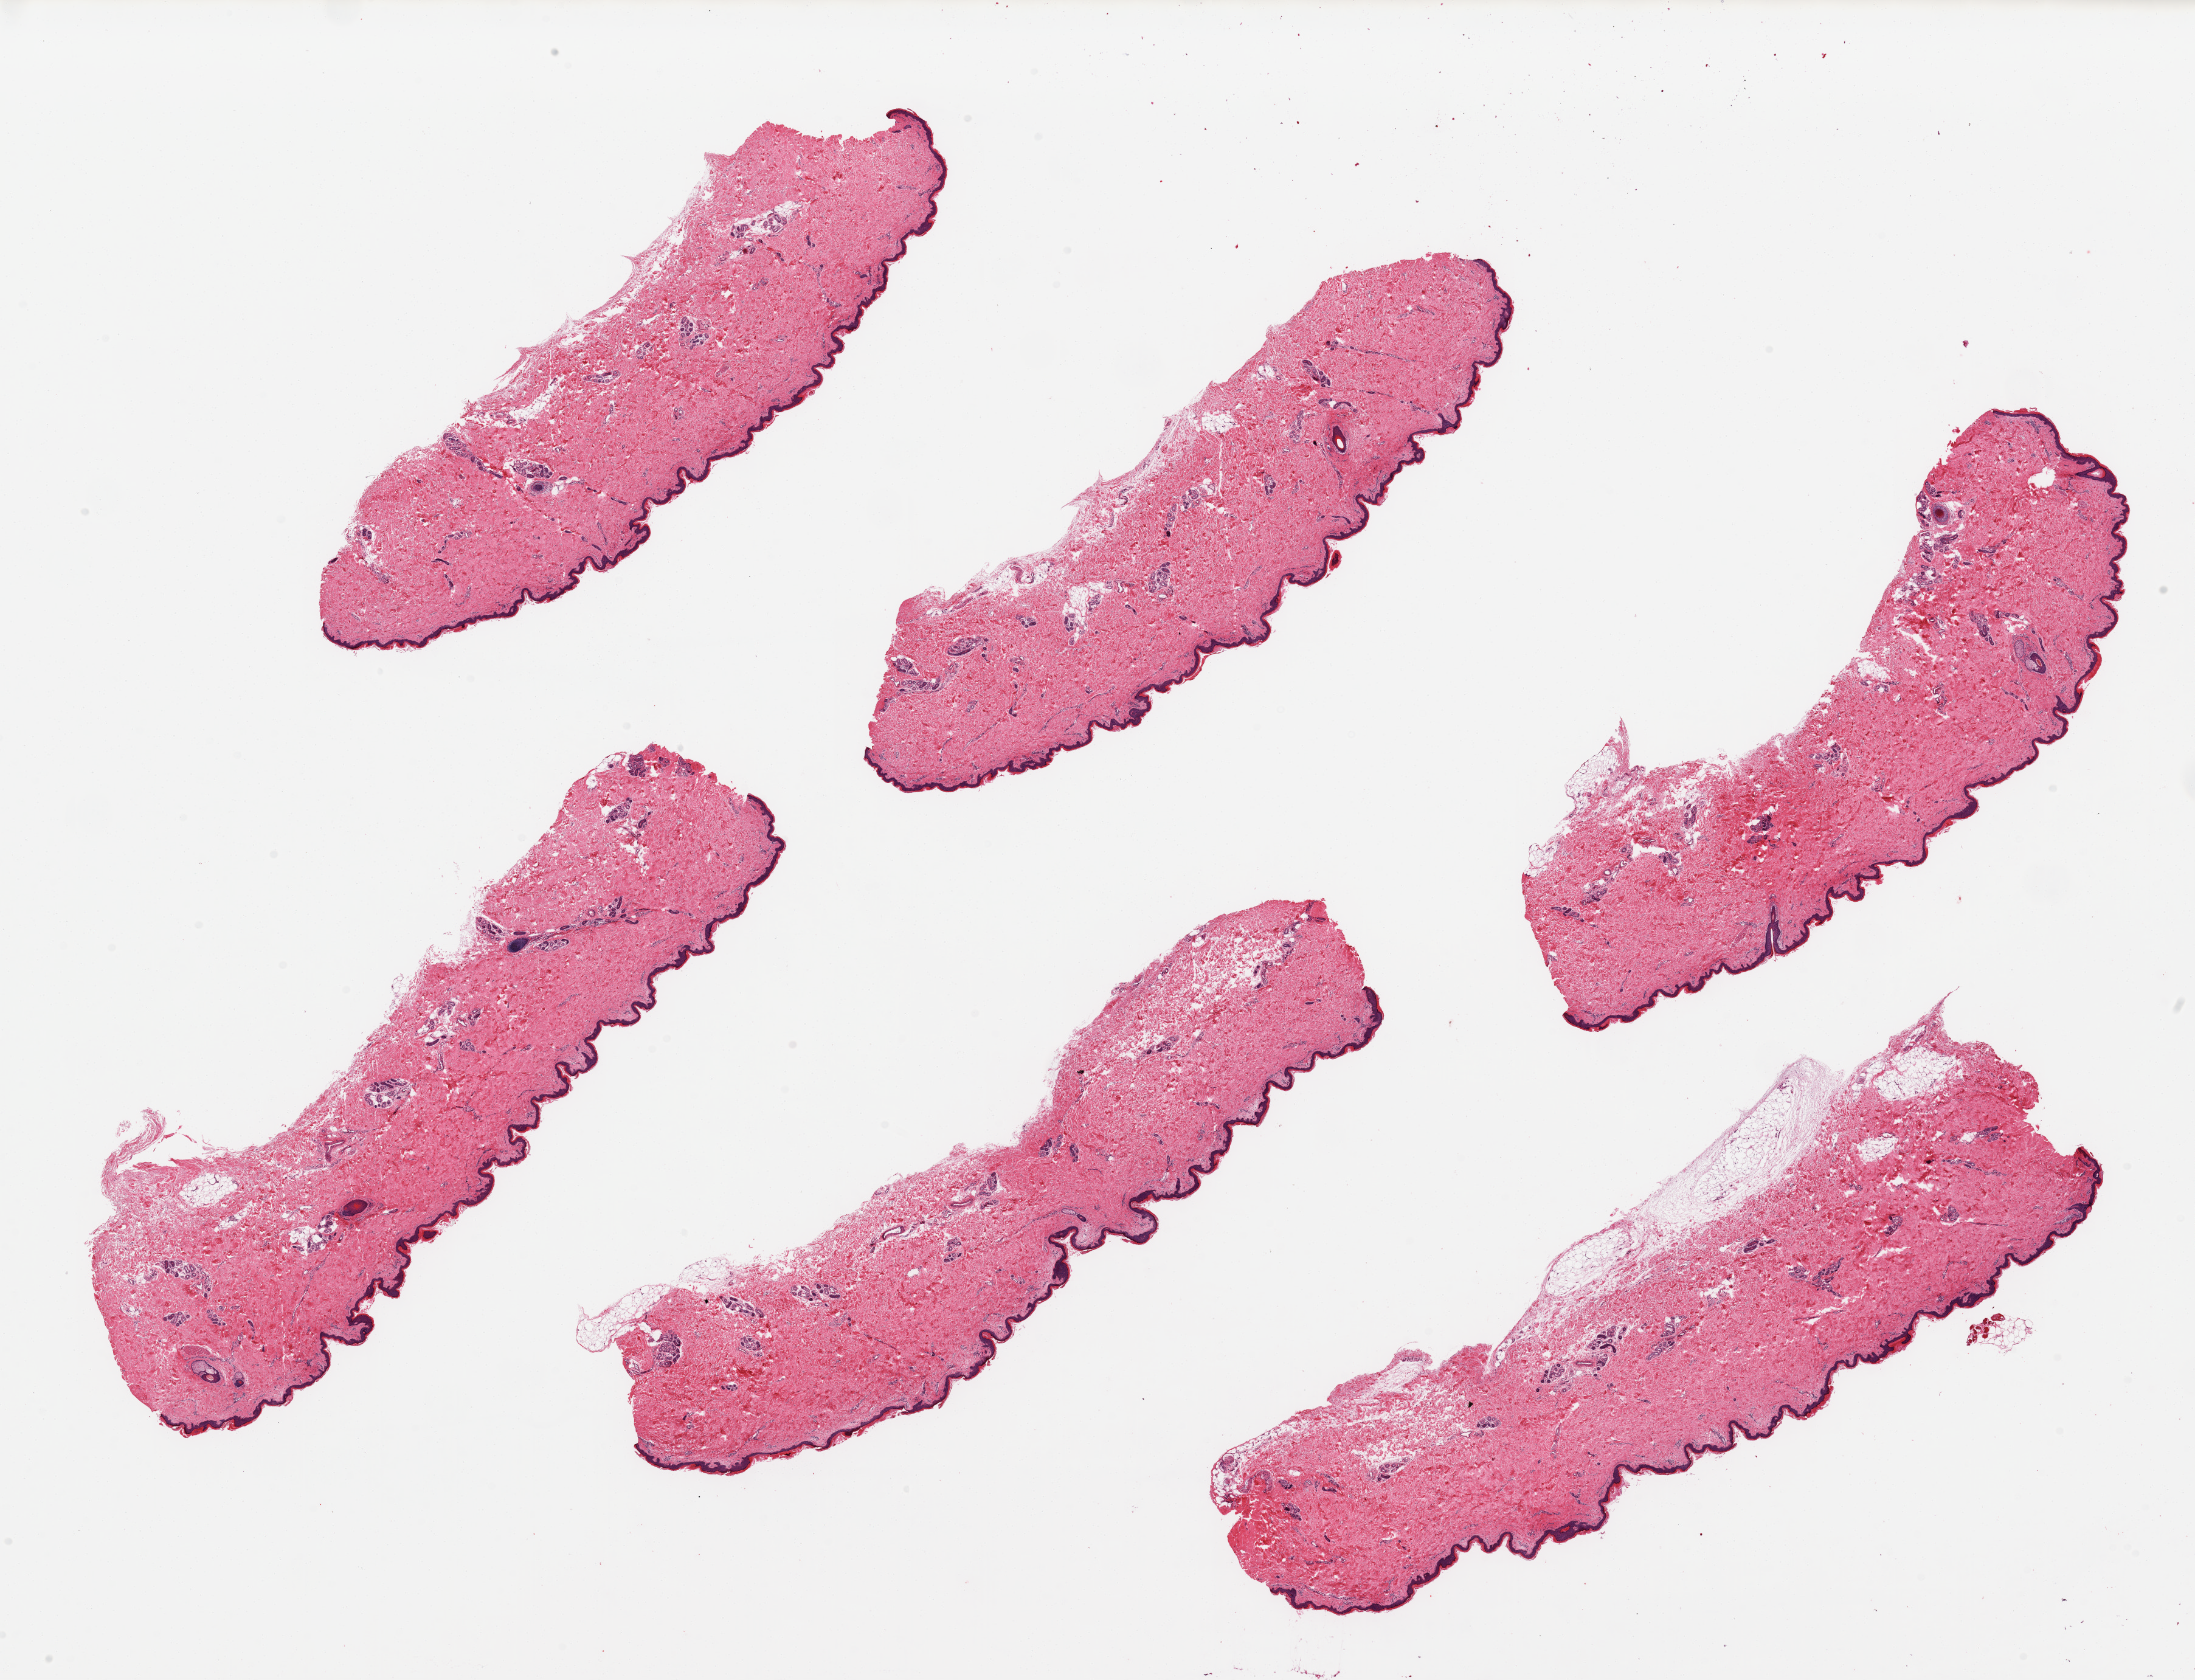
Digitized H&E-stained section, brightfield — a low-resolution overview of the entire scanned area, about 28.5 x 21.9 mm (slide scanned at 20x), PAXgene-fixed paraffin-embedded (PFPE) section, target tissue: skin of lower leg, donor tissue sample. Donor sex: male.
Review note (as recorded): 6 pieces; mostly well trimmed with minimal internal/external fat, 1 with ~10% attached fat, epidermis measures 41 microns.